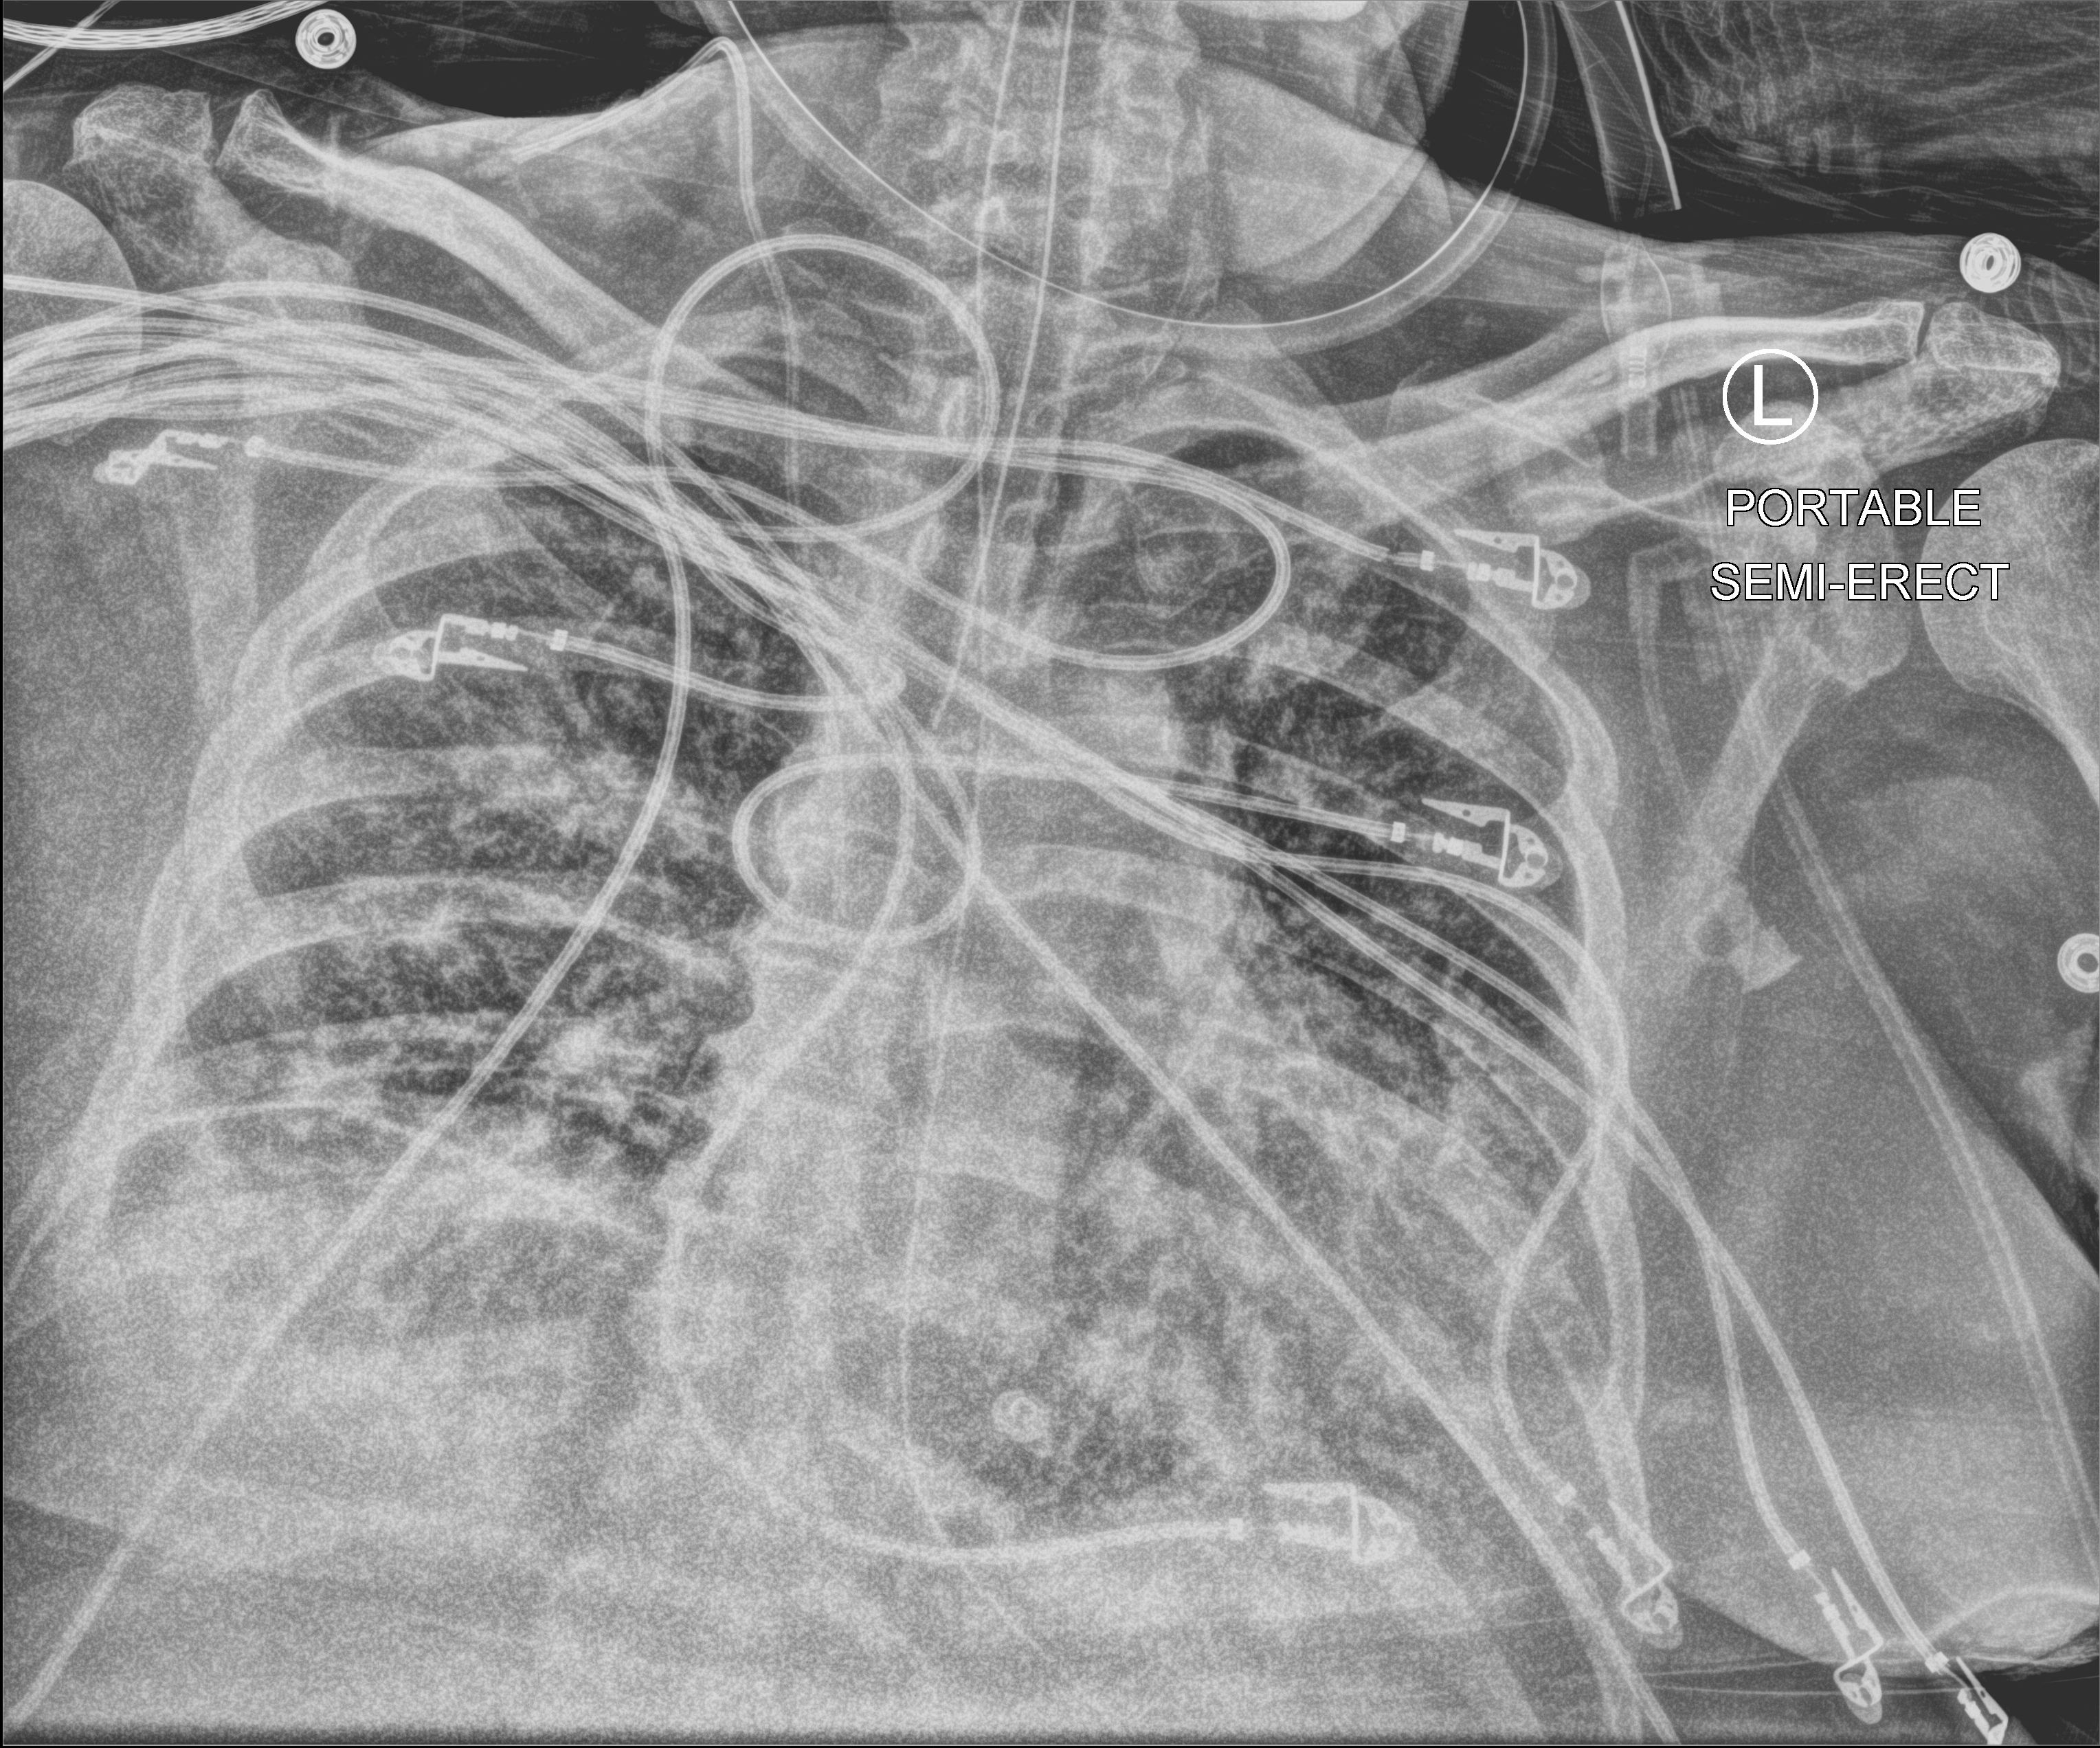
Bedside chest radiograph (computed radiography). Male patient hospitalised with COVID-19, age 60–74 years.
From the hospital-stay record, not from the radiograph (when in the stay this image was taken is not recorded): admitted to intensive care during this hospital stay: yes.